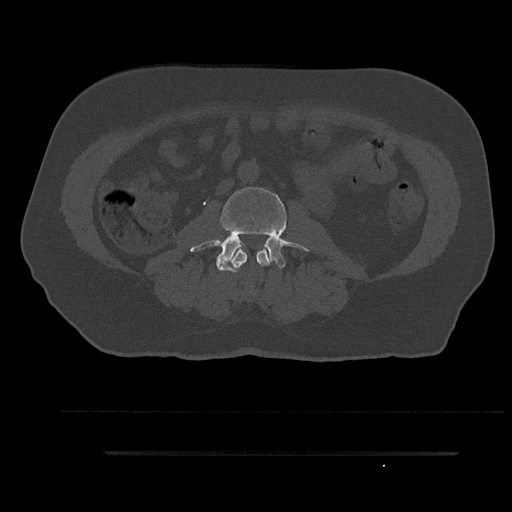
CT including the spine, one axial slice. Slice 64 of 797 in the series (ordered by position). Reconstruction kernel Br40s/3. 120 kVp. Bone window (W 1800 / L 400 HU). 0.5 mm slice thickness. 512 × 512 image matrix, field of view 432 × 432 mm. Male patient, age 63 years. From the clinical record (not read from this slice): primary cancer: renal; vertebrae with lytic lesions (as recorded): T8.
Annotated regions visible in this slice (semi-automatic segmentation, software-assisted and operator-edited):
- L2 vertebra: bounding box <231,249,270,288> (left, top, right, bottom; pixels)
- L3 vertebra: <190,185,307,272>